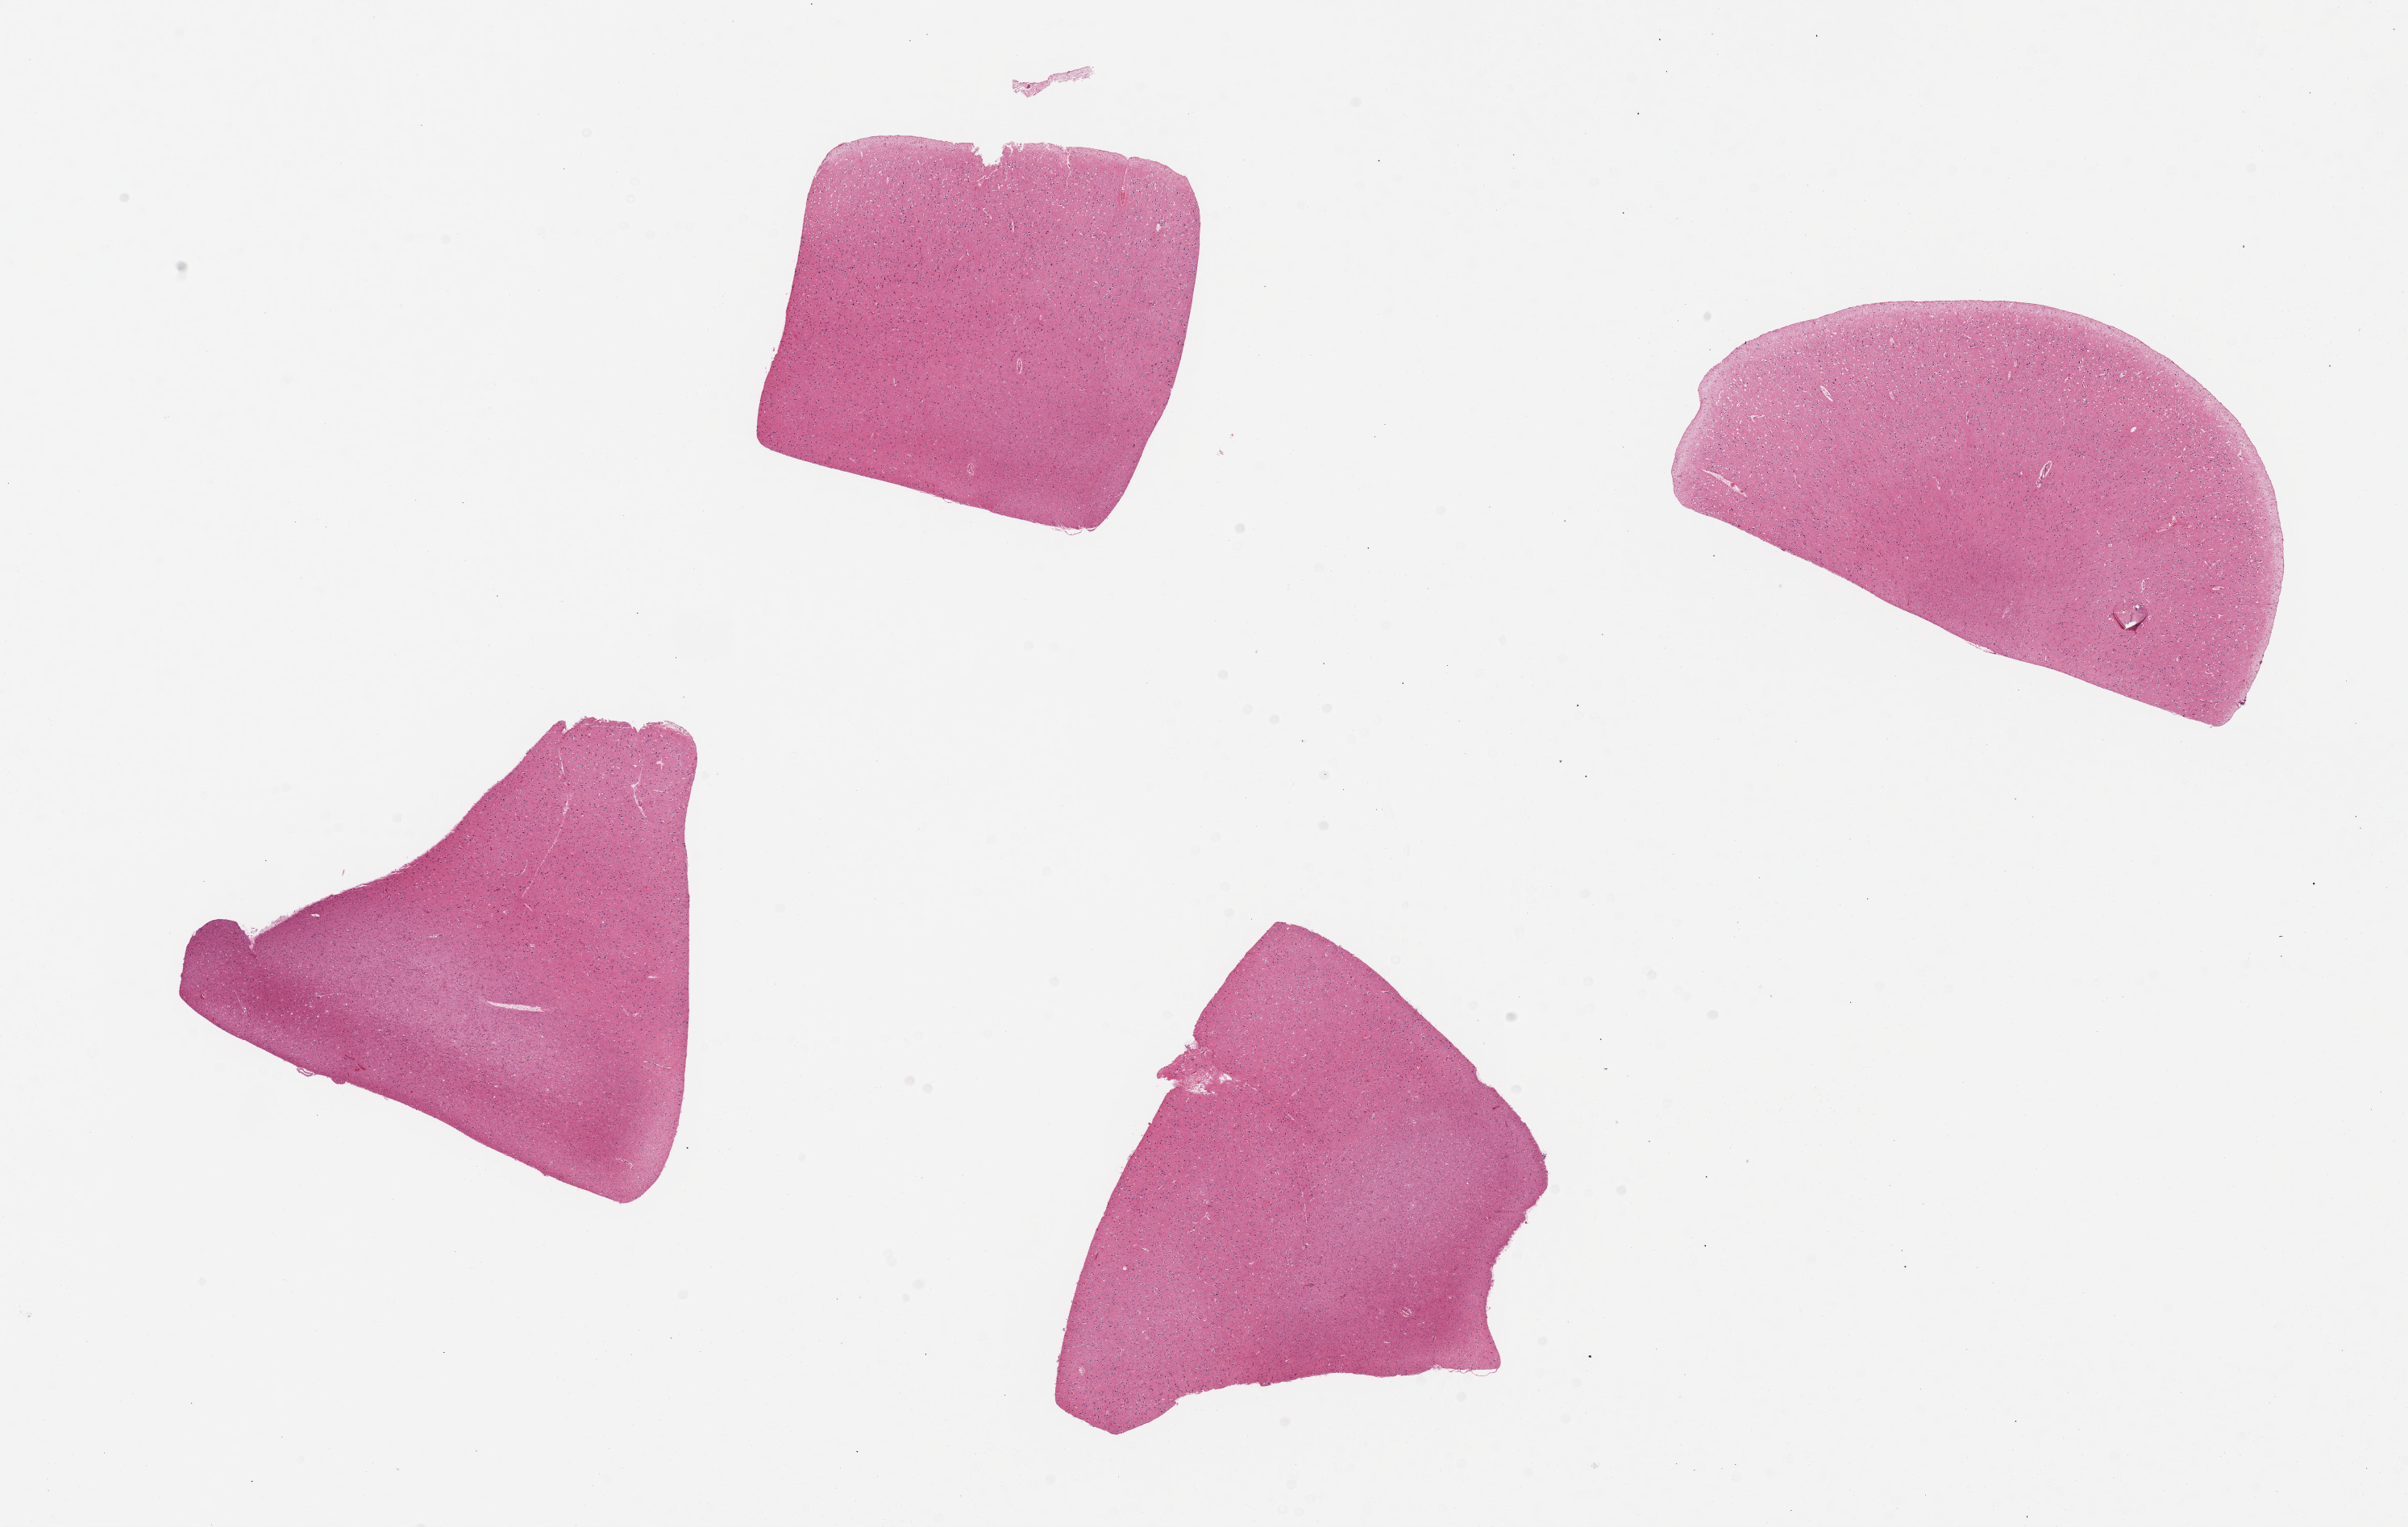
Digitized haematoxylin and eosin-stained section — whole scanned area (about 23.6 x 15.0 mm, acquisition: 20x scan) shown as a low-resolution overview, PAXgene-fixed, paraffin-embedded tissue, section of cerebral cortex (target tissue), donor tissue sample.
Review note (as recorded): 4 pieces.